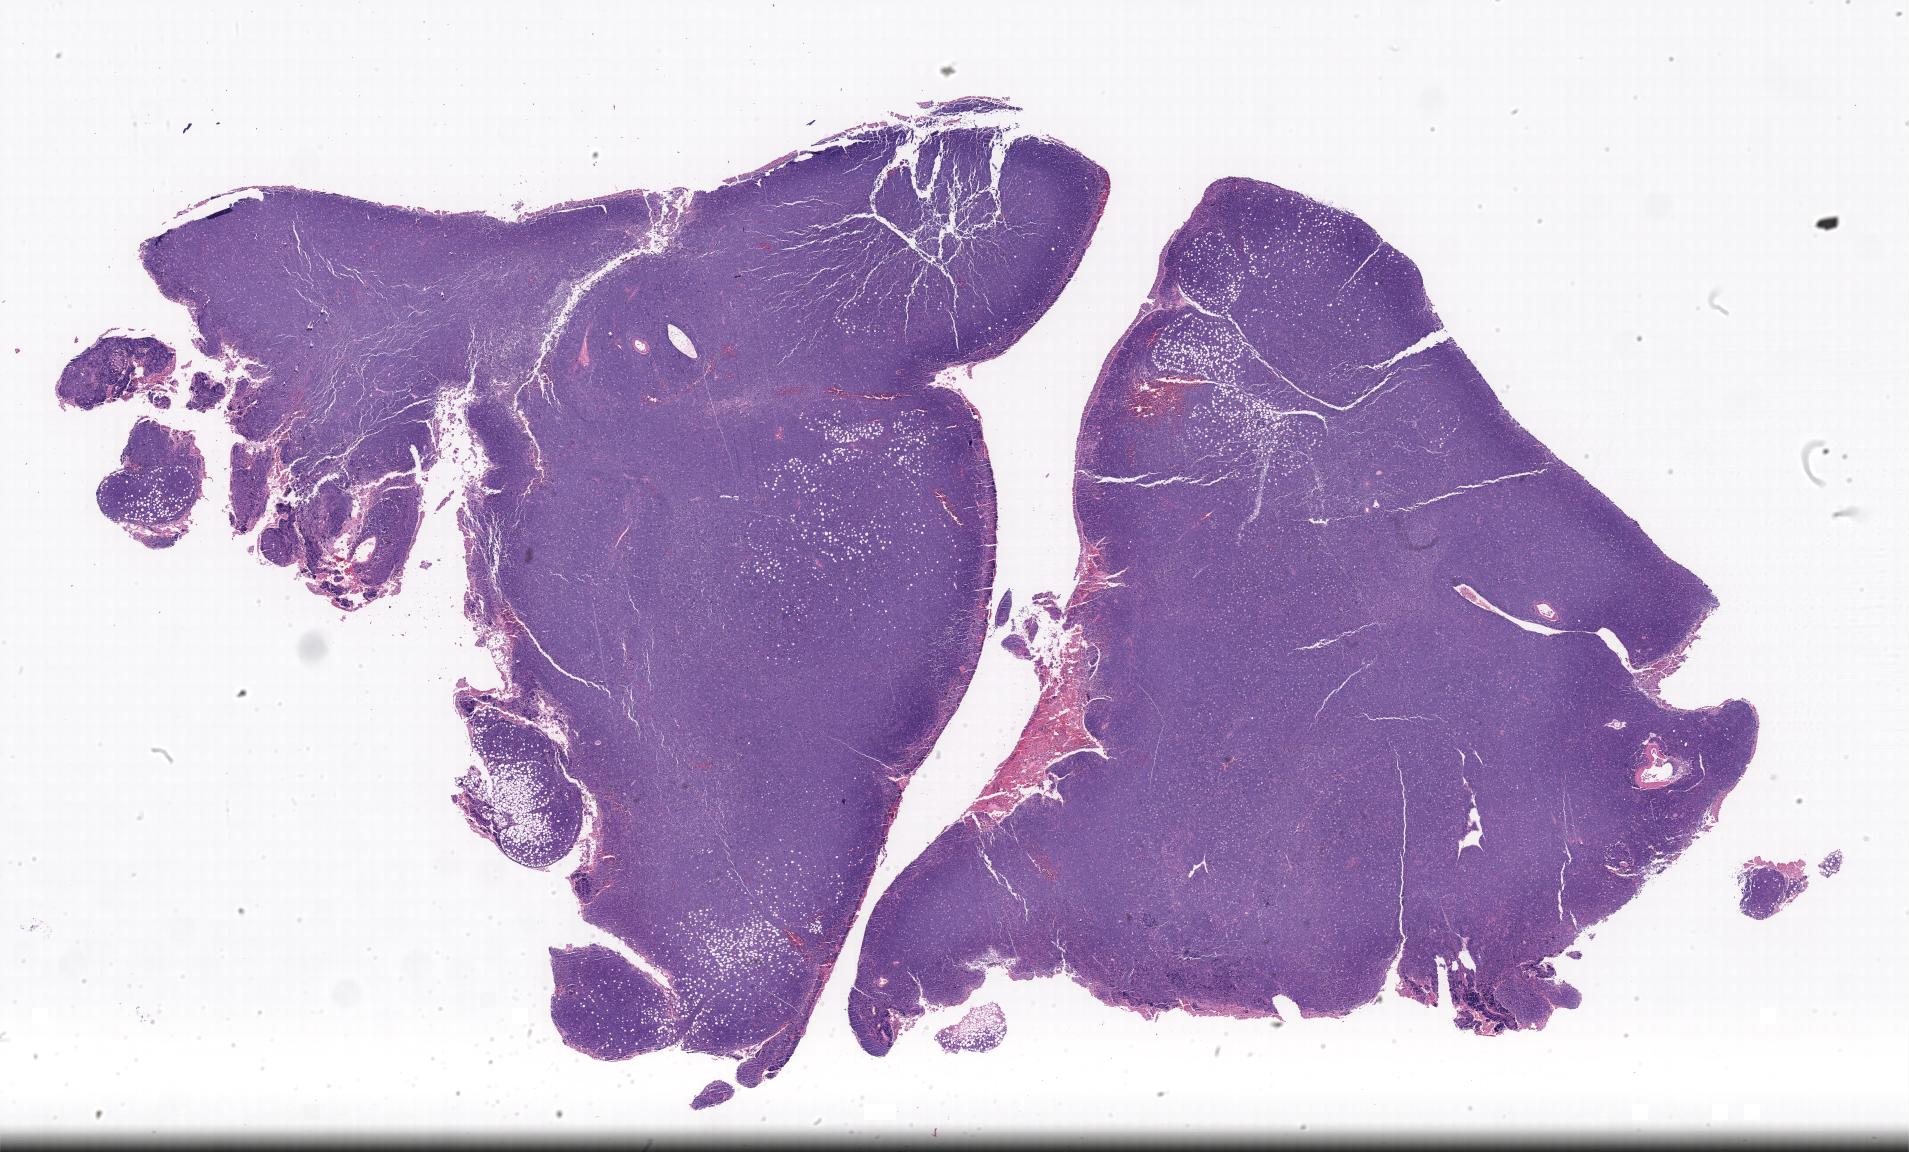
Hematoxylin and eosin (H&E) whole-slide image, a low-resolution overview of the entire scanned area. Tumor tissue. Site: peritoneum. Male, age 9 years at initial diagnosis.
Diagnosis: Burkitt lymphoma, NOS.